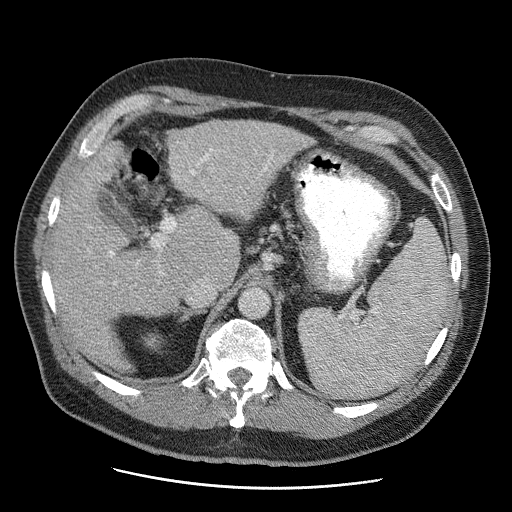
Contrast-enhanced abdominal CT (liver protocol), one axial slice; slice 32 of 81 in the series (ordered by position); reconstruction kernel STANDARD; soft-tissue window (W 400 / L 40 HU); 2.5 mm slice thickness; 512 × 512 image matrix, field of view 380 × 380 mm. From the clinical record (not read from this slice): diagnosis: hepatocellular carcinoma (patient treated with transarterial chemoembolisation; whether this scan precedes or follows treatment is not stated here); TNM stage (as recorded): Stage-IIIA; Child-Pugh class: A; tumour differentiation: moderately differentiated; tumour nodularity: multinodular.
Outlined on this slice (semi-automatic segmentation, software-assisted and operator-edited):
- abdominal aorta: bounding box [x1, y1, x2, y2] px = [239, 288, 269, 318]
- liver parenchyma outside the tumour (the mass and vessels are separate outlines, so this box may not span the whole liver): [50, 120, 310, 363]
- liver vessels: [110, 149, 267, 255]